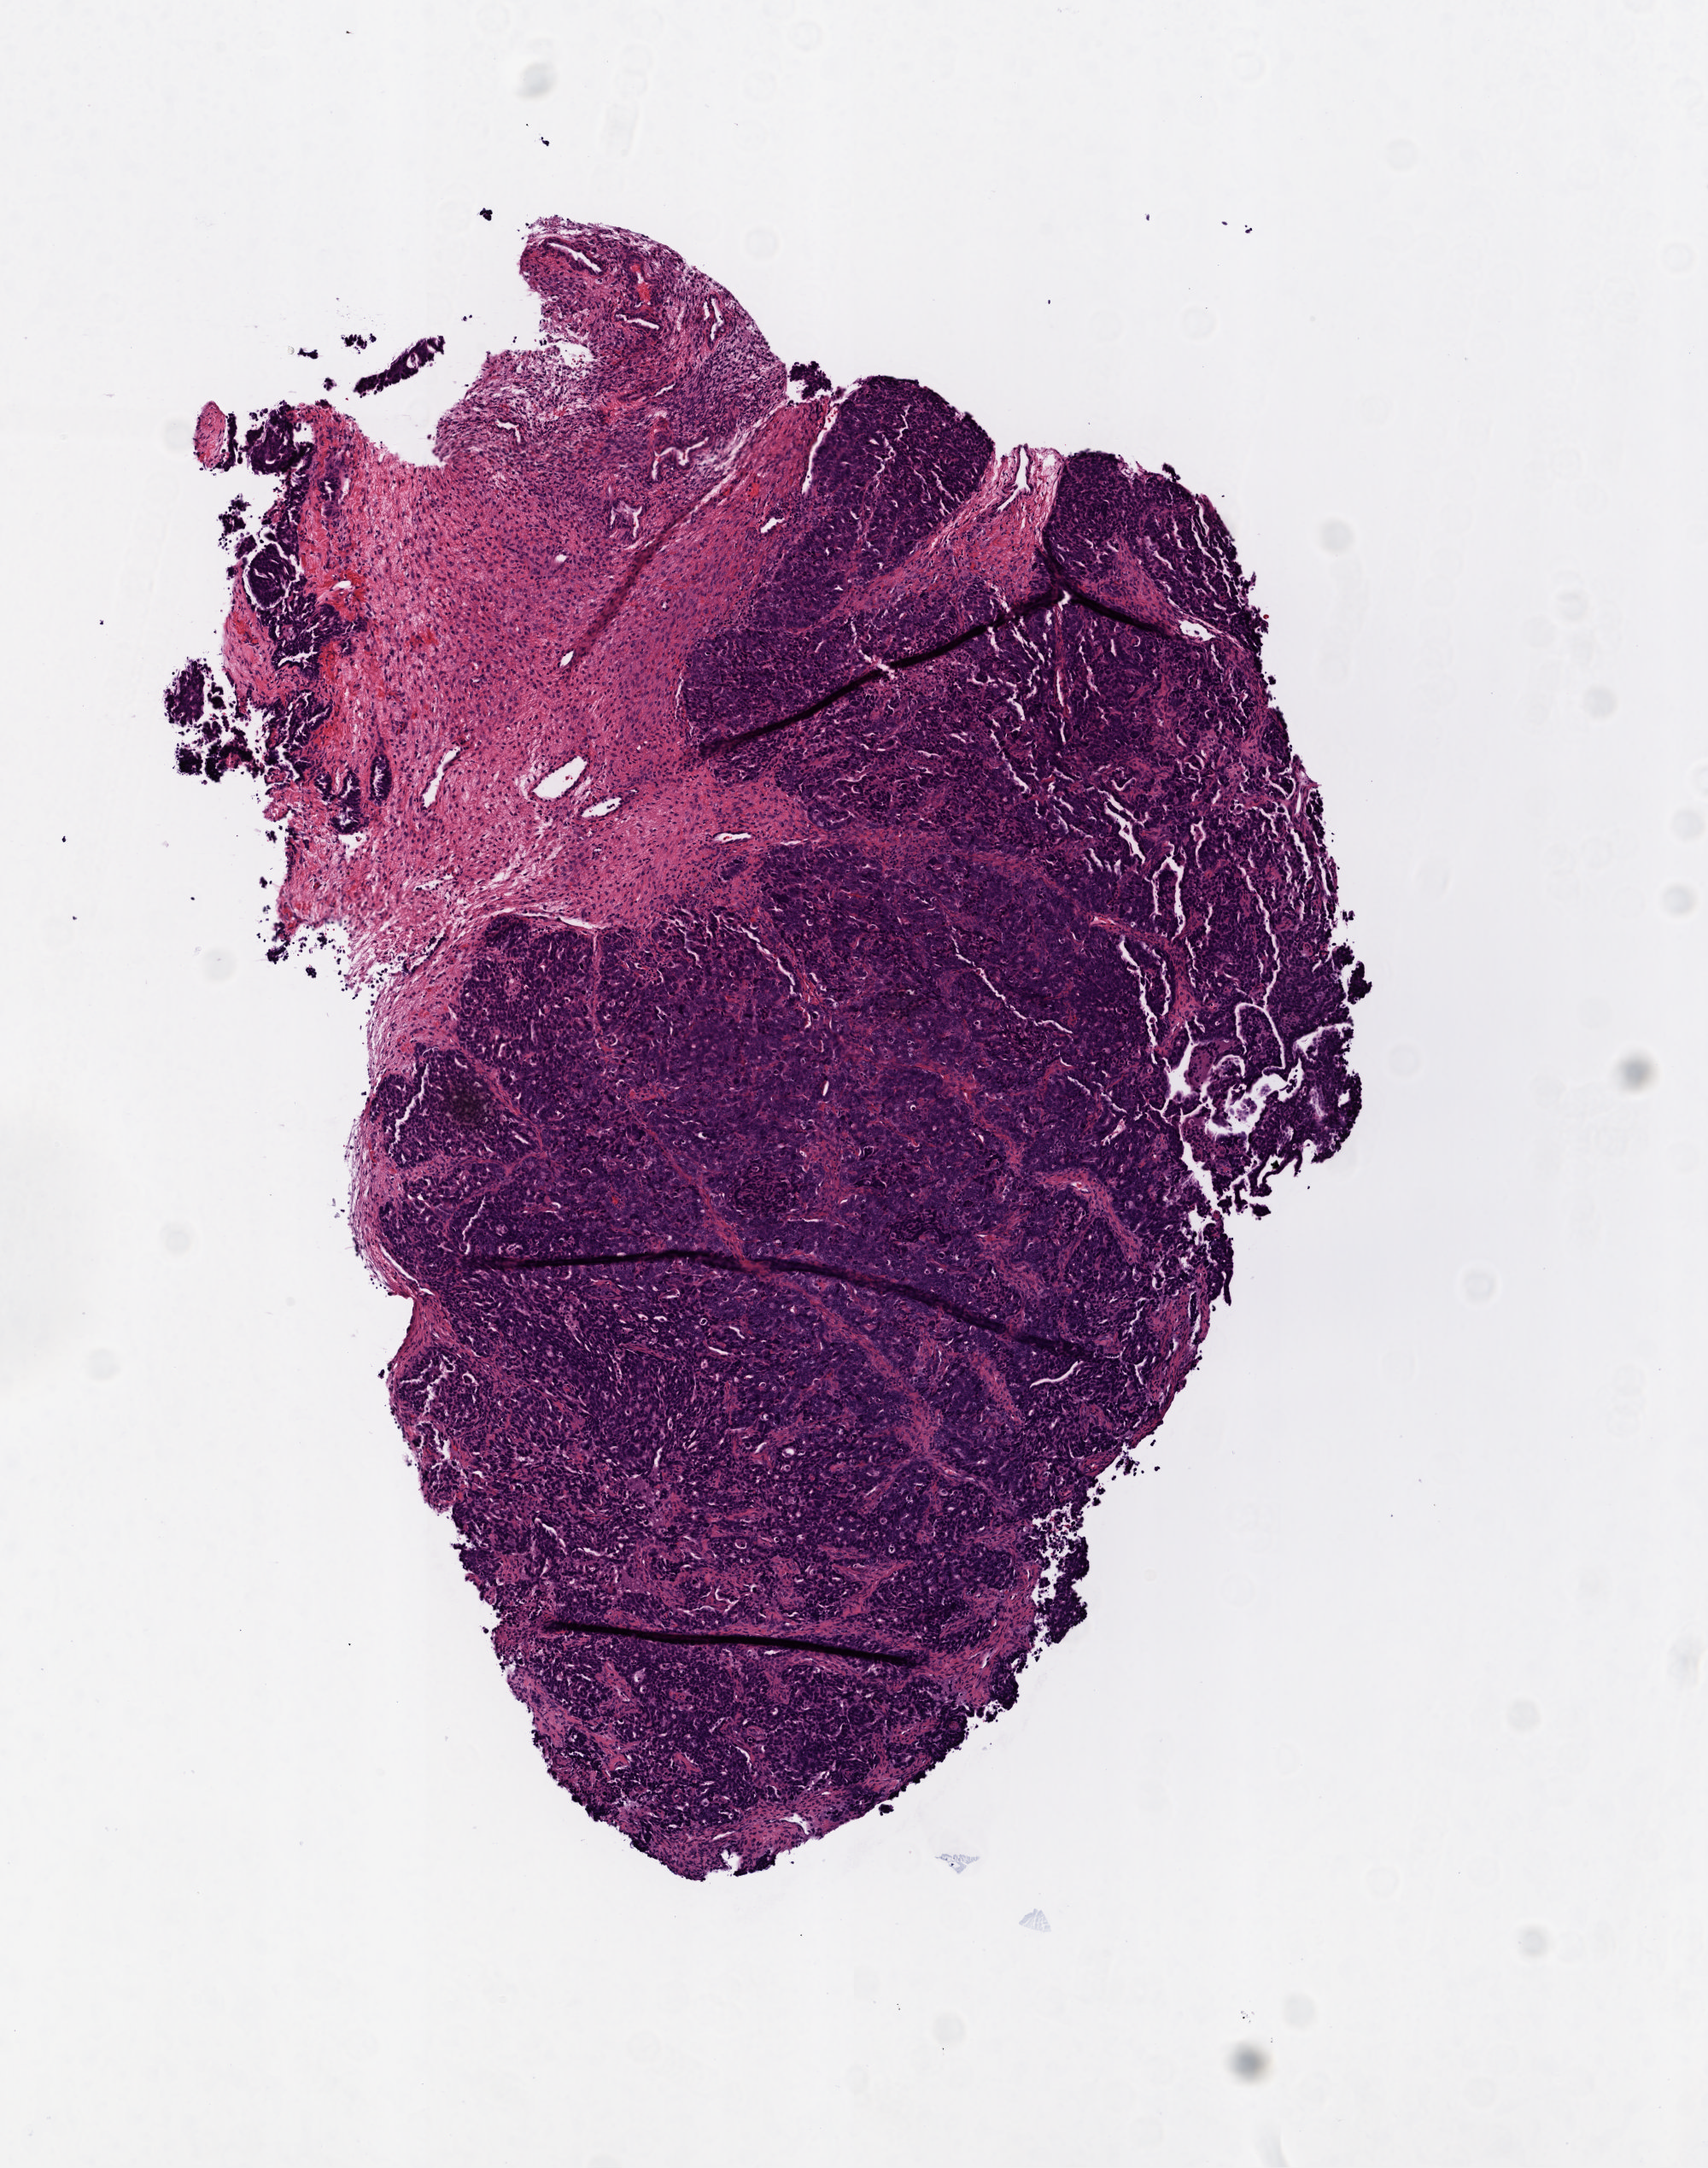
Digitized Hematoxylin and eosin (H&E) stained tissue section (whole slide), low-resolution overview of the scanned area, about 4.0 x 5.1 mm (from a 20x scan); frozen section; primary tumour sample from the ovary. Female, age 67 years at initial diagnosis. Histologic grade: G3 (poorly differentiated). Composition of this section per pathologist review: tumour cells 70%, tumour nuclei 90%, normal cells 0%, stromal cells 30%, necrosis 0%.
Pathologic diagnosis: Serous cystadenocarcinoma, NOS. FIGO stage: IIIC.